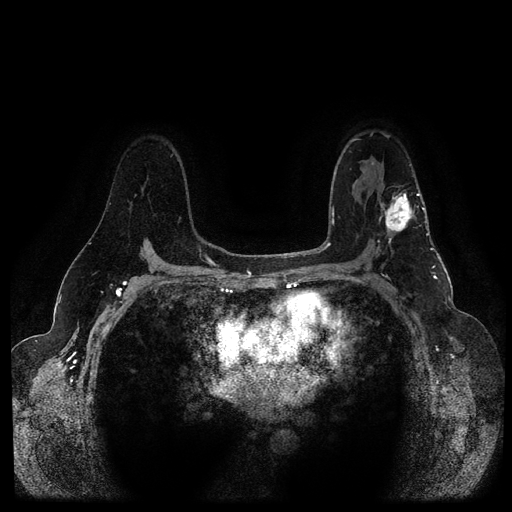
Breast MRI (dynamic contrast-enhanced, multi-phase), one axial slice. Position 71 of 116 along the scan axis. Dynamic contrast-enhanced series, time point 2 of 5 at this slice position (early post-contrast). 1.5 T. TE 2.6 ms, TR 5.3 ms. 2 mm slice thickness. 512 × 512 image matrix, field of view 350 × 350 mm. Patient: female, 54 years.
Annotated regions visible in this slice (semi-automatic segmentation, software-assisted and operator-edited):
- breast lesion (labelled 'tumour' in the annotation; benign lesions carry a separate 'benign' label): box from (x=377, y=186) to (x=419, y=237) px